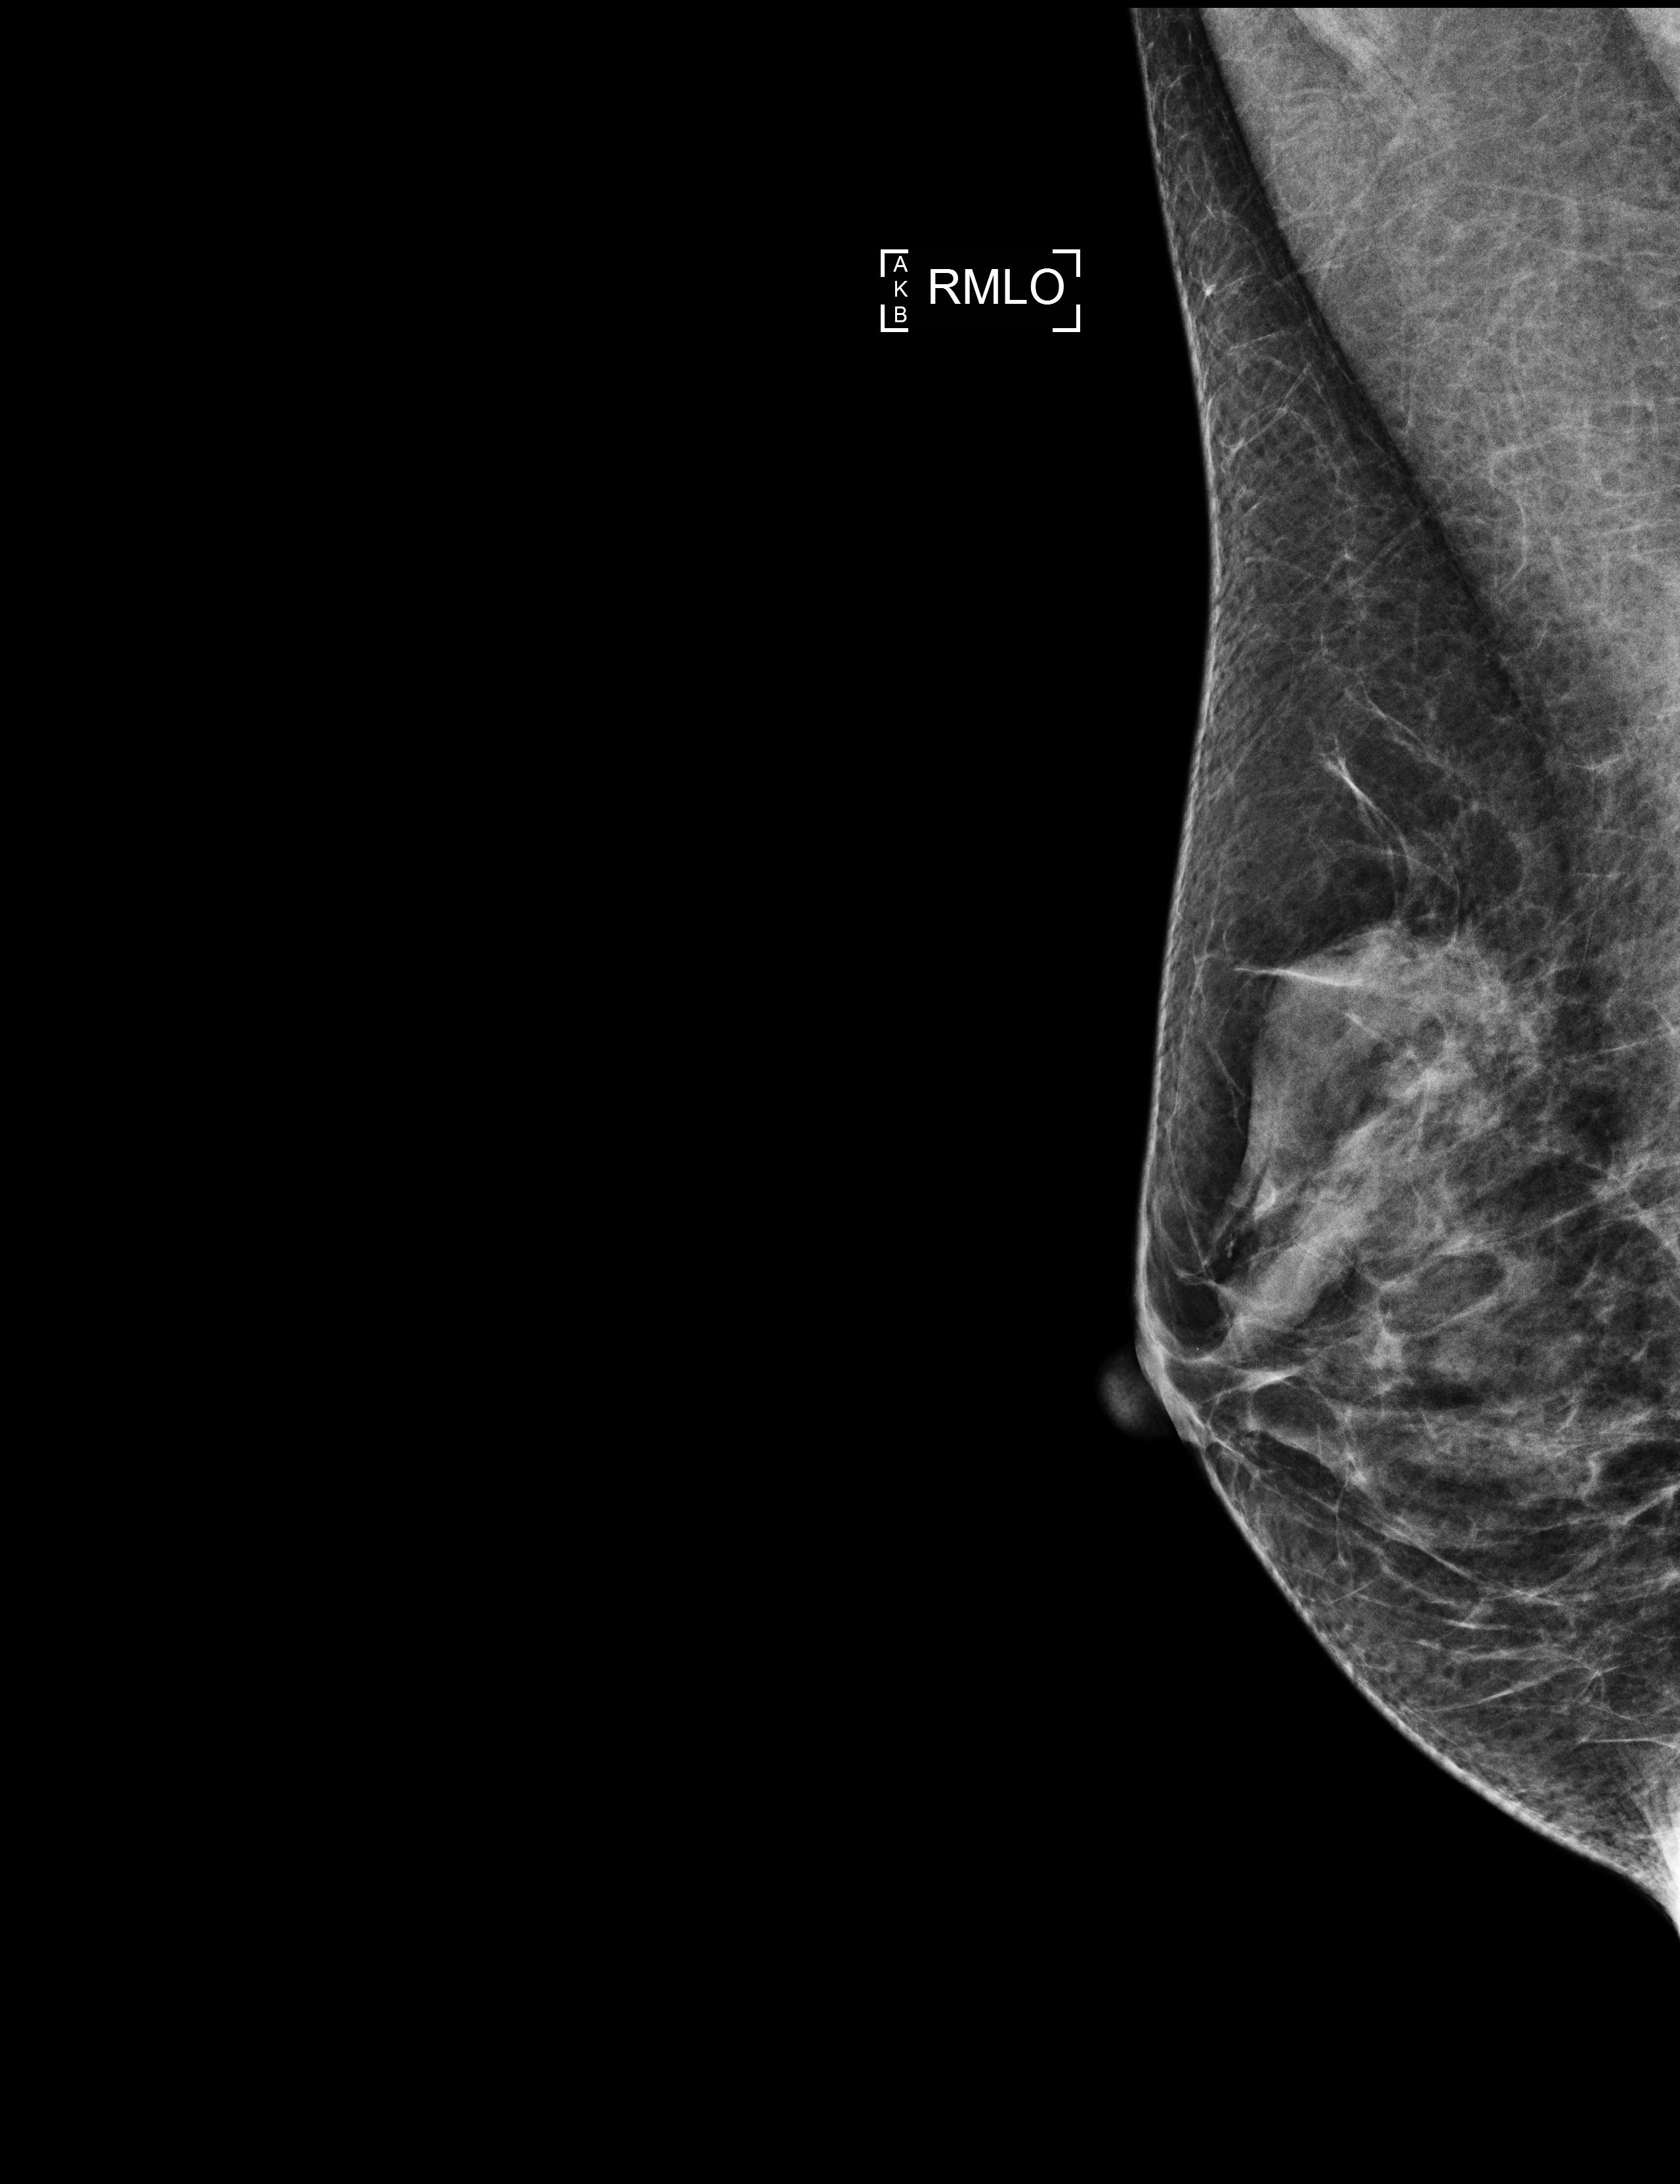
Digital mammogram (FFDM); right breast; medio-lateral oblique projection; screening examination; compressed breast thickness 36 mm. Patient aged 57 years (female).
BI-RADS breast density category at the screening exam (both breasts, scale 1–4): 3. Final BI-RADS category for the screening round (tomosynthesis exam, both breasts): category 1. Recall: no recall after this screen.